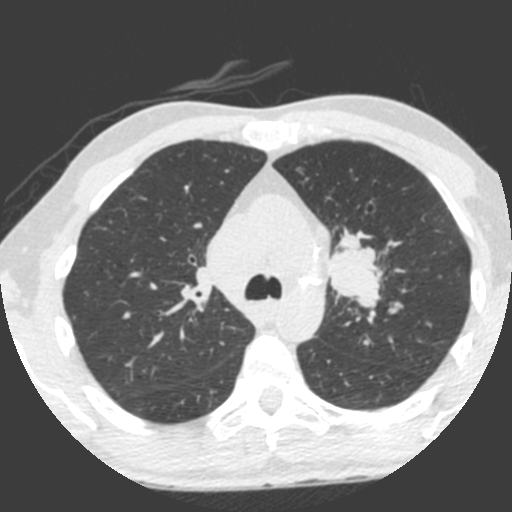
Low-dose screening chest CT, one axial slice. Slice 150 of 212 in the series (ordered by position). 120 kVp. Lung window (W 1500 / L -600 HU). 512 × 512 image matrix.
Annotated regions visible in this slice (outlined manually by an expert reader):
- lesion 1 (tumor, upper lobe of left lung): bounding box (x1, y1, x2, y2) in pixels: (328, 230, 383, 310)